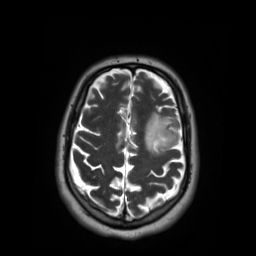
Brain MRI from a brain-tumour surgery series, one axial slice. Position 42 of 59 along the scan axis. 3.03 mm slice thickness. 256 × 256 image matrix. From the clinical record (not read from this slice): histopathology: Oligodendroglioma; WHO grade: 2; IDH mutation: yes.
Structures marked on this image (outlined manually by an expert reader):
- tumour: box from (x=144, y=112) to (x=178, y=155) px